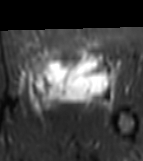
MRI of an extremity soft-tissue mass, one axial slice; slice 38 of 81 in the series (ordered by position); STIR; MR volume resampled by the dataset authors to the PET/CT grid (not the native acquisition matrix); 3.27 mm slice thickness; 143 × 161 image matrix, field of view 140 × 157 mm. Female patient. From the clinical record (not read from this slice): histological type: myxofibrosarcoma; grade: intermediate; site of the primary tumour: left thigh.
Annotated regions visible in this slice (expert contour drawn on MRI and transferred to this co-registered scan by the dataset authors):
- gross tumour volume including surrounding oedema: box from (x=26, y=49) to (x=118, y=114) px
- gross tumour volume (mass): (x=33, y=49)–(x=107, y=100)